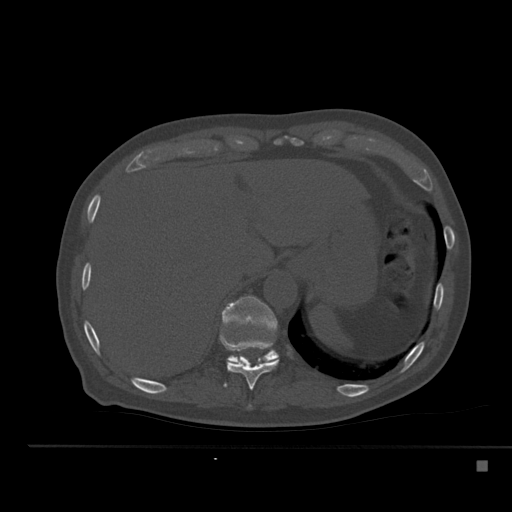
CT including the spine, one axial slice. Reconstruction kernel Br40s. Bone window (W 1800 / L 400 HU). 1.5 mm slice thickness. 512 × 512 image matrix, field of view 408 × 408 mm. Patient: male, 70 years. Case-level facts recorded for this patient, not image findings: primary cancer: renal.
Outlined on this slice (semi-automatically segmented with operator editing):
- T10 vertebra: bounding box (x1, y1, x2, y2) in pixels: (219, 335, 279, 390)
- T11 vertebra: (222, 296, 279, 363)
- T9 vertebra: (249, 406, 251, 408)